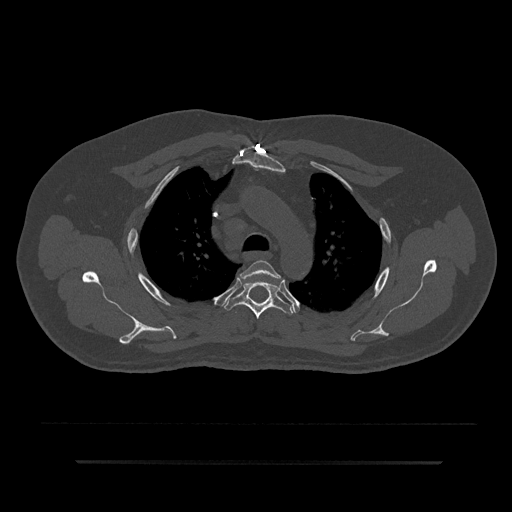
CT including the spine, one axial slice. Position 628 of 797 along the scan axis. 120 kVp. Bone window (W 1800 / L 400 HU). 0.5 mm slice thickness. 512 × 512 image matrix. Male patient, age 59 years. Case-level facts recorded for this patient, not image findings: primary cancer: bile ducts; vertebrae with lytic lesions (as recorded): T10.
Annotated regions visible in this slice (semi-automatically segmented with operator editing):
- T3 vertebra: bounding box <240,260,283,282> (left, top, right, bottom; pixels)
- T4 vertebra: <223,277,294,319>